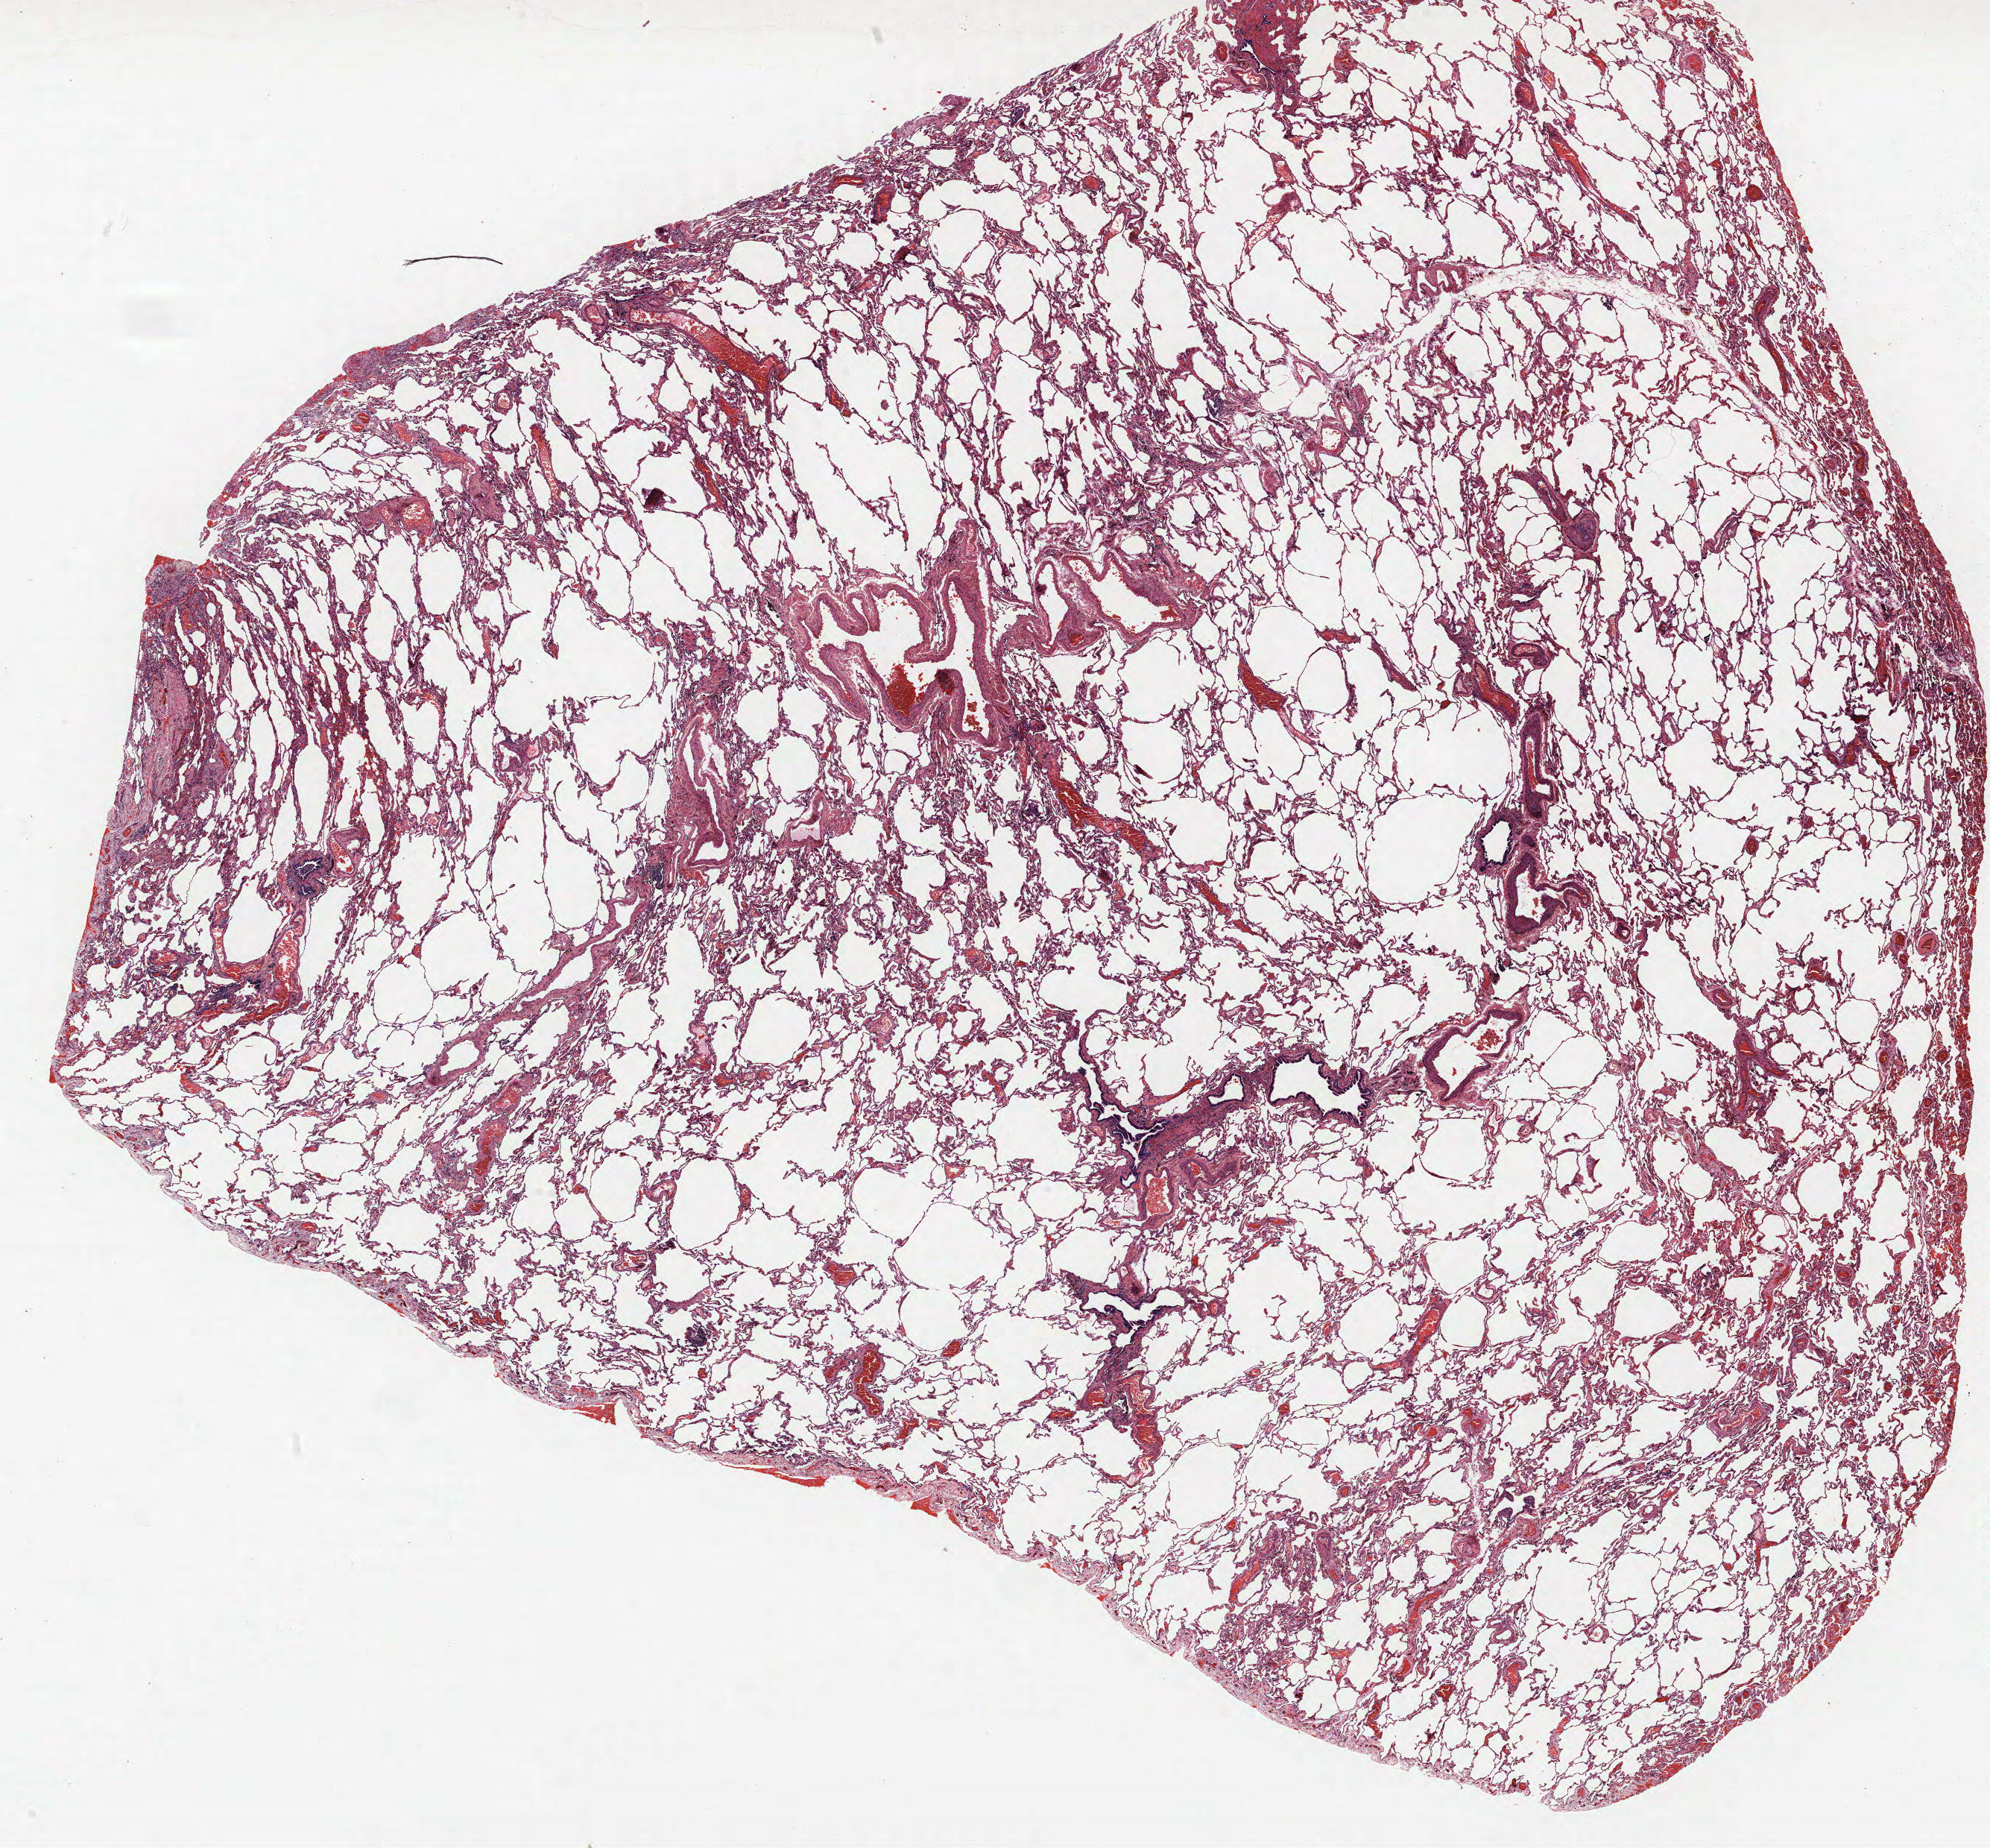
Whole-slide histology image, H&E, shown as a low-resolution overview of the whole scanned area (about 21.4 x 19.8 mm, from a 40x scan), FFPE section, lung tissue. Female patient, aged 56 at enrolment. Former smoker at enrolment. Grade: well differentiated (G1).
Participant's lung-cancer diagnosis: Bronchiolo-alveolar carcinoma, non-mucinous. Primary tumour location (clinical record): left upper lobe. Stage (AJCC 6th edition): IA. Tumour size (pathology): 25 mm.